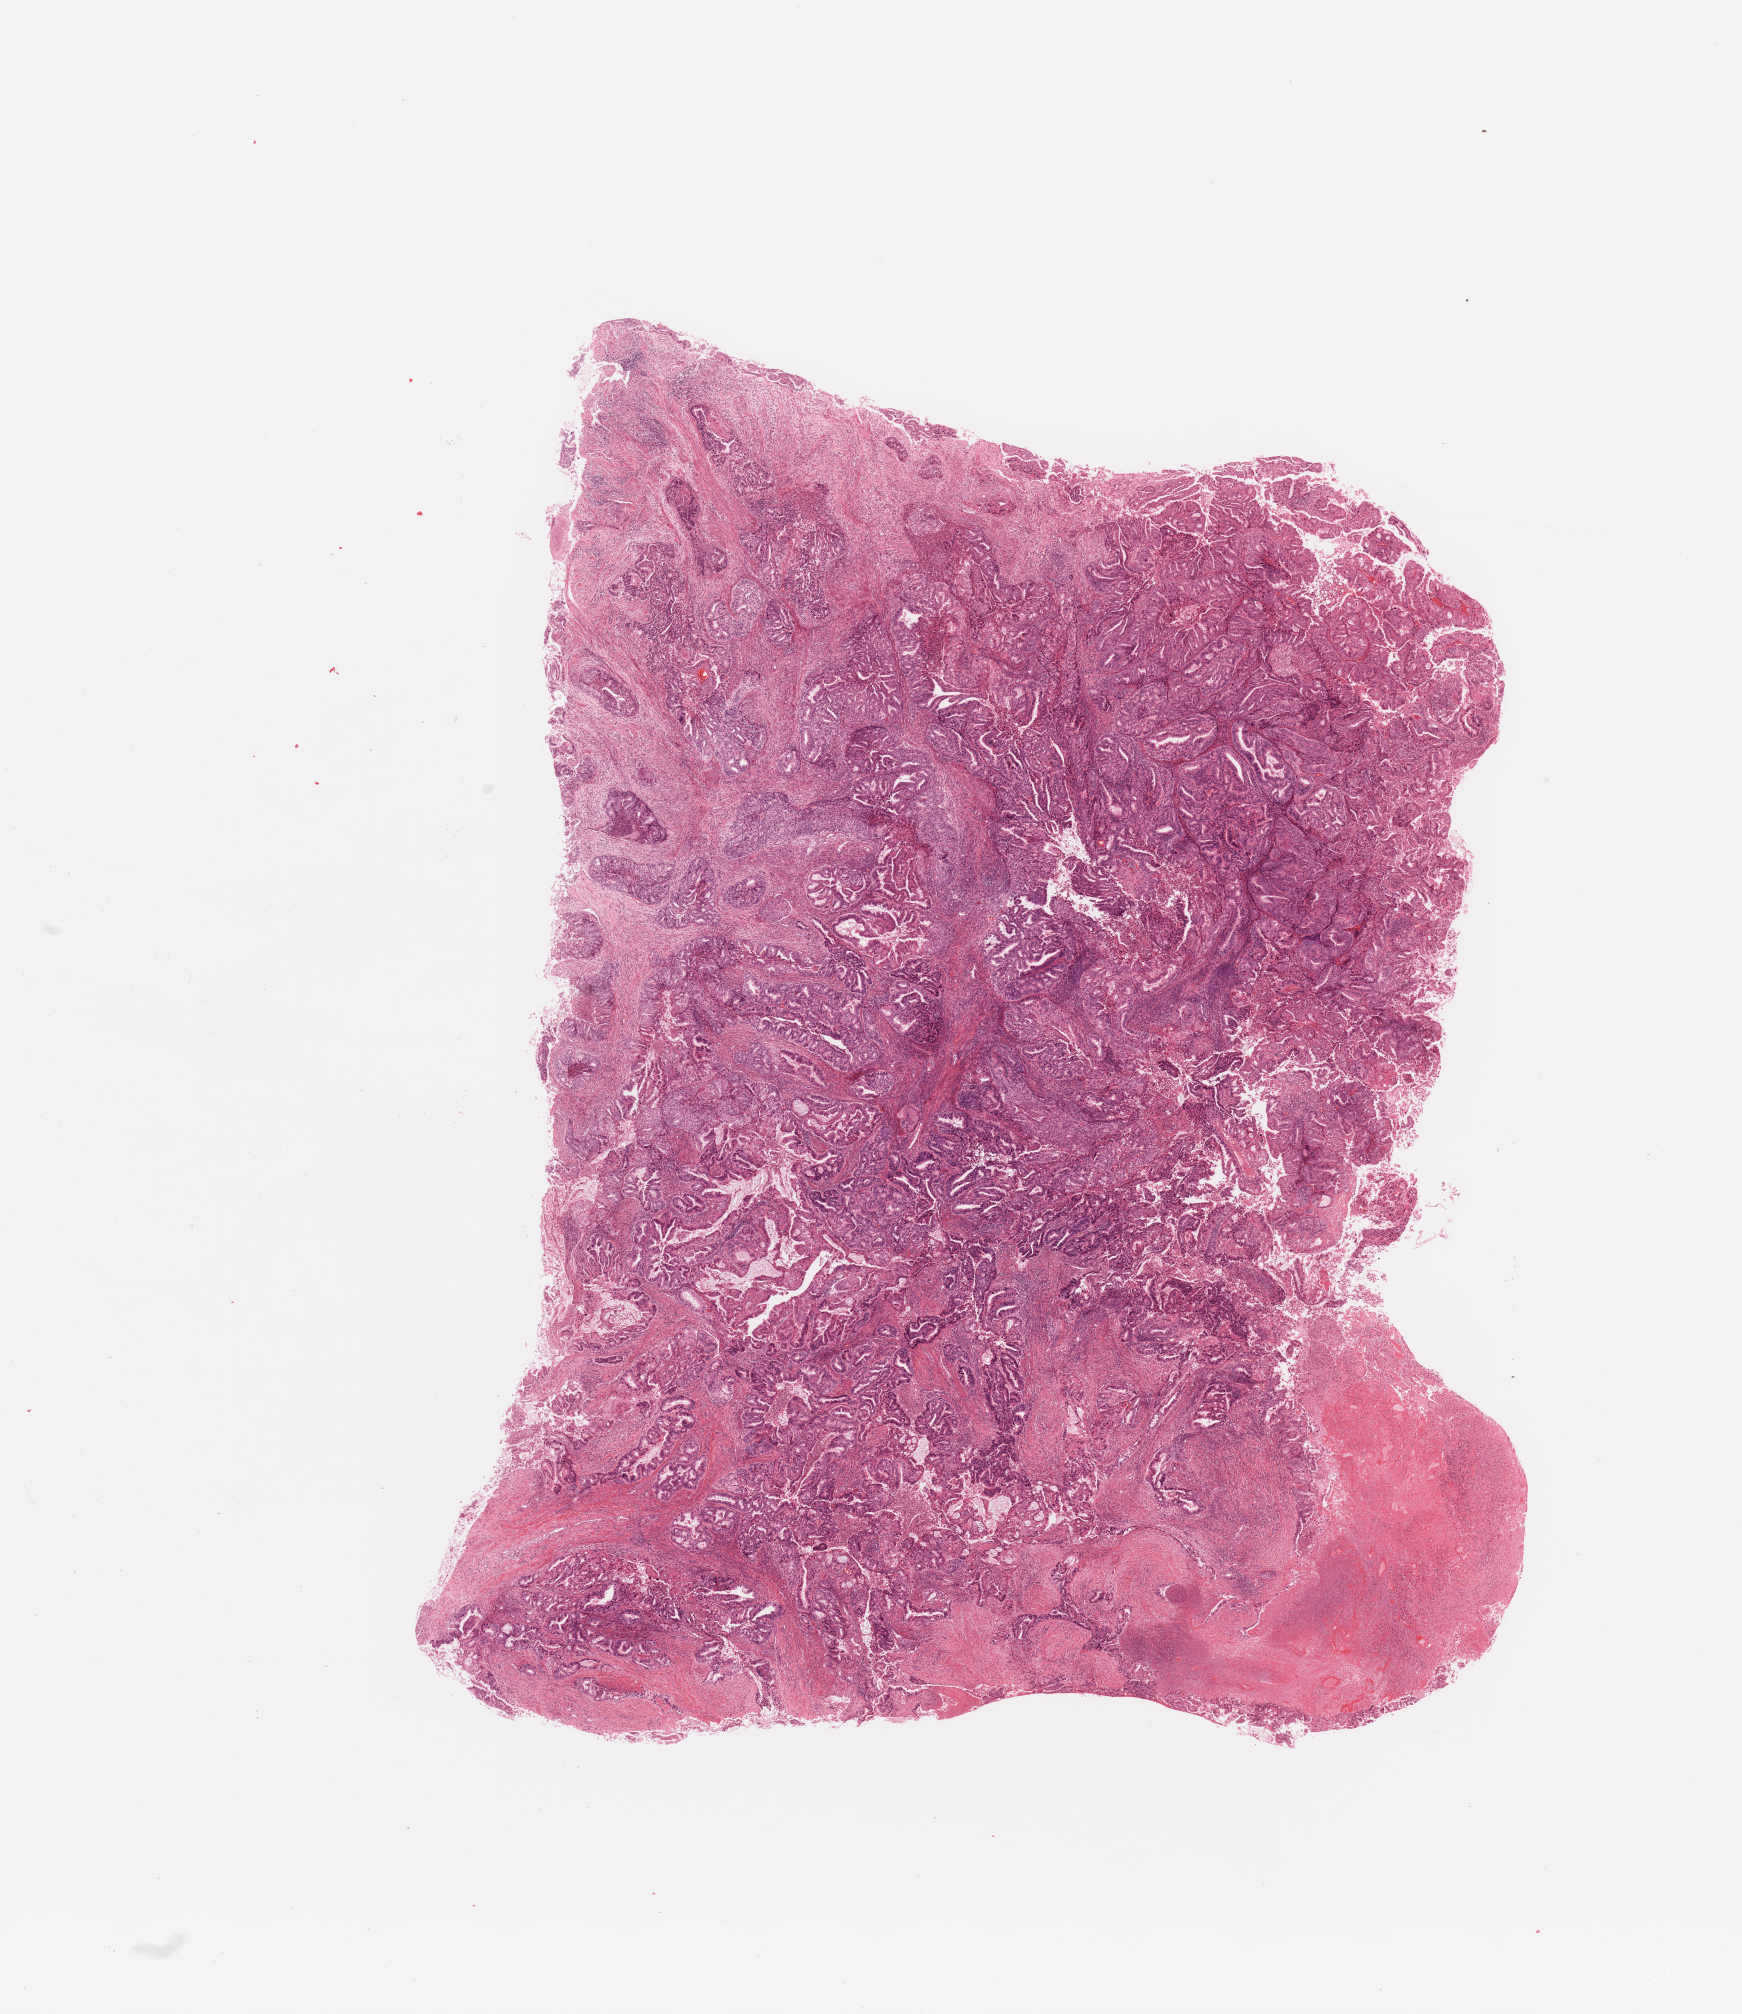
Whole-slide histology image, H&E, low-resolution overview of the scanned area, about 13.8 x 15.9 mm; tumour tissue sample, uterus. 60-year-old female patient. Histologic grade: G3 (poorly differentiated).
- AJCC pathologic stage: I
- histologic diagnosis: Endometrioid adenocarcinoma, NOS